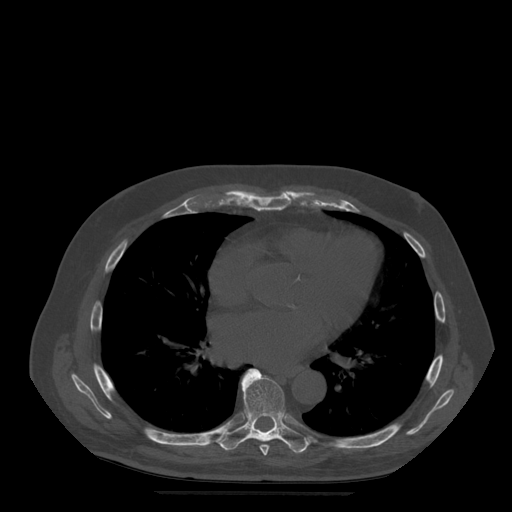
CT including the spine, one axial slice; slice 317 of 522 in the series (ordered by position); bone window (W 1800 / L 400 HU); 512 × 512 image matrix, field of view 420 × 420 mm. Patient age 72 years. Case-level facts recorded for this patient, not image findings: primary cancer: prostate.
Structures marked on this image (semi-automatically segmented with operator editing):
- T7 vertebra: box from (x=260, y=445) to (x=270, y=456) px
- T8 vertebra: (x=217, y=369)–(x=311, y=454)